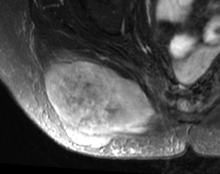
MRI of an extremity soft-tissue mass, one axial slice. Slice 25 of 63 in the series (ordered by position). T2-weighted fat-saturated. MR volume resampled by the dataset authors to the PET/CT grid (not the native acquisition matrix). 220 × 174 image matrix, field of view 215 × 170 mm. Female patient. Case-level facts recorded for this patient, not image findings: histological type: spindle cell suggestive of myxofibrosarcoma; grade: intermediate; site of the primary tumour: right buttock.
Outlined on this slice (expert contour drawn on MRI and transferred to this co-registered scan by the dataset authors):
- gross tumour volume (mass): bounding box (x1, y1, x2, y2) in pixels: (43, 52, 156, 149)